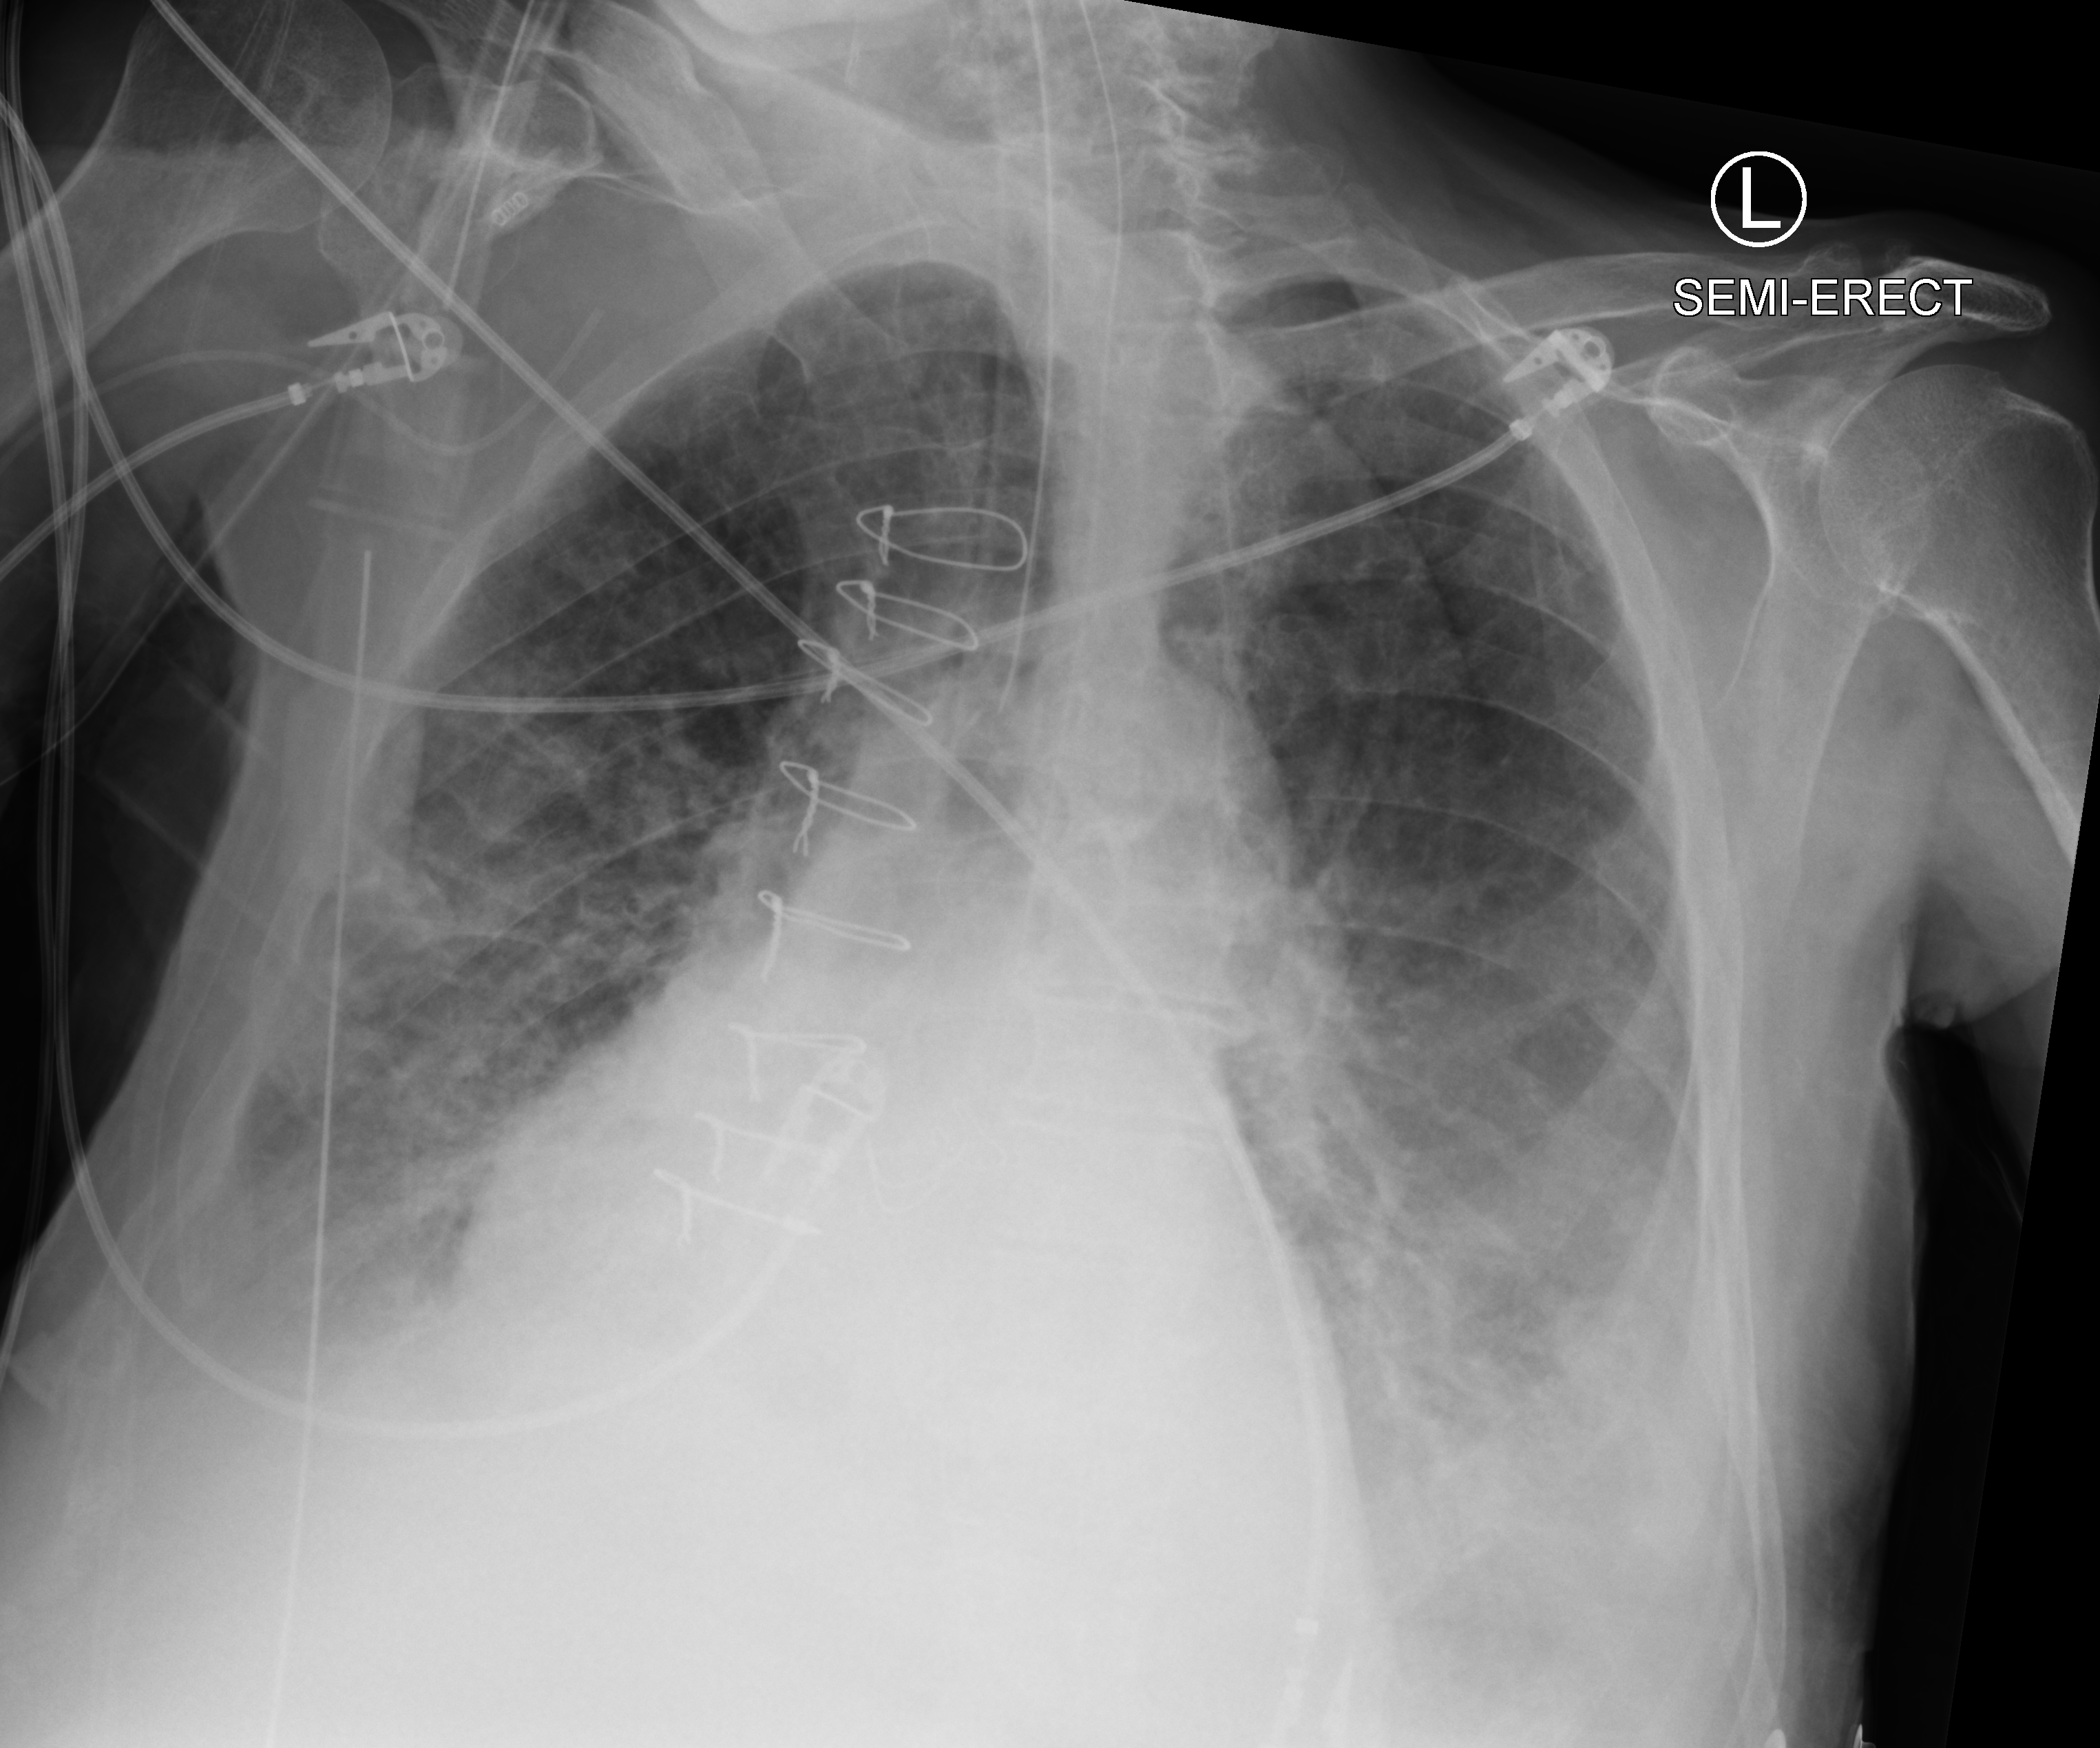
Chest X-ray (portable). Male patient hospitalised with COVID-19, age 75–90 years.
From the hospital-stay record, not from the radiograph (when in the stay this image was taken is not recorded):
- mechanically ventilated during this hospital stay: yes
- length of hospital stay: 40 days